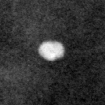
Crop from a digitized film mammogram around one marked abnormality, left breast, CC view, BI-RADS breast density category 1 (scale 1–4).
Marked abnormality: calcifications, morphology lucent center; BI-RADS assessment category 2; subtlety rating 5 on a 1 (subtle) to 5 (obvious) scale; benign; no additional work-up was recommended (benign without callback).